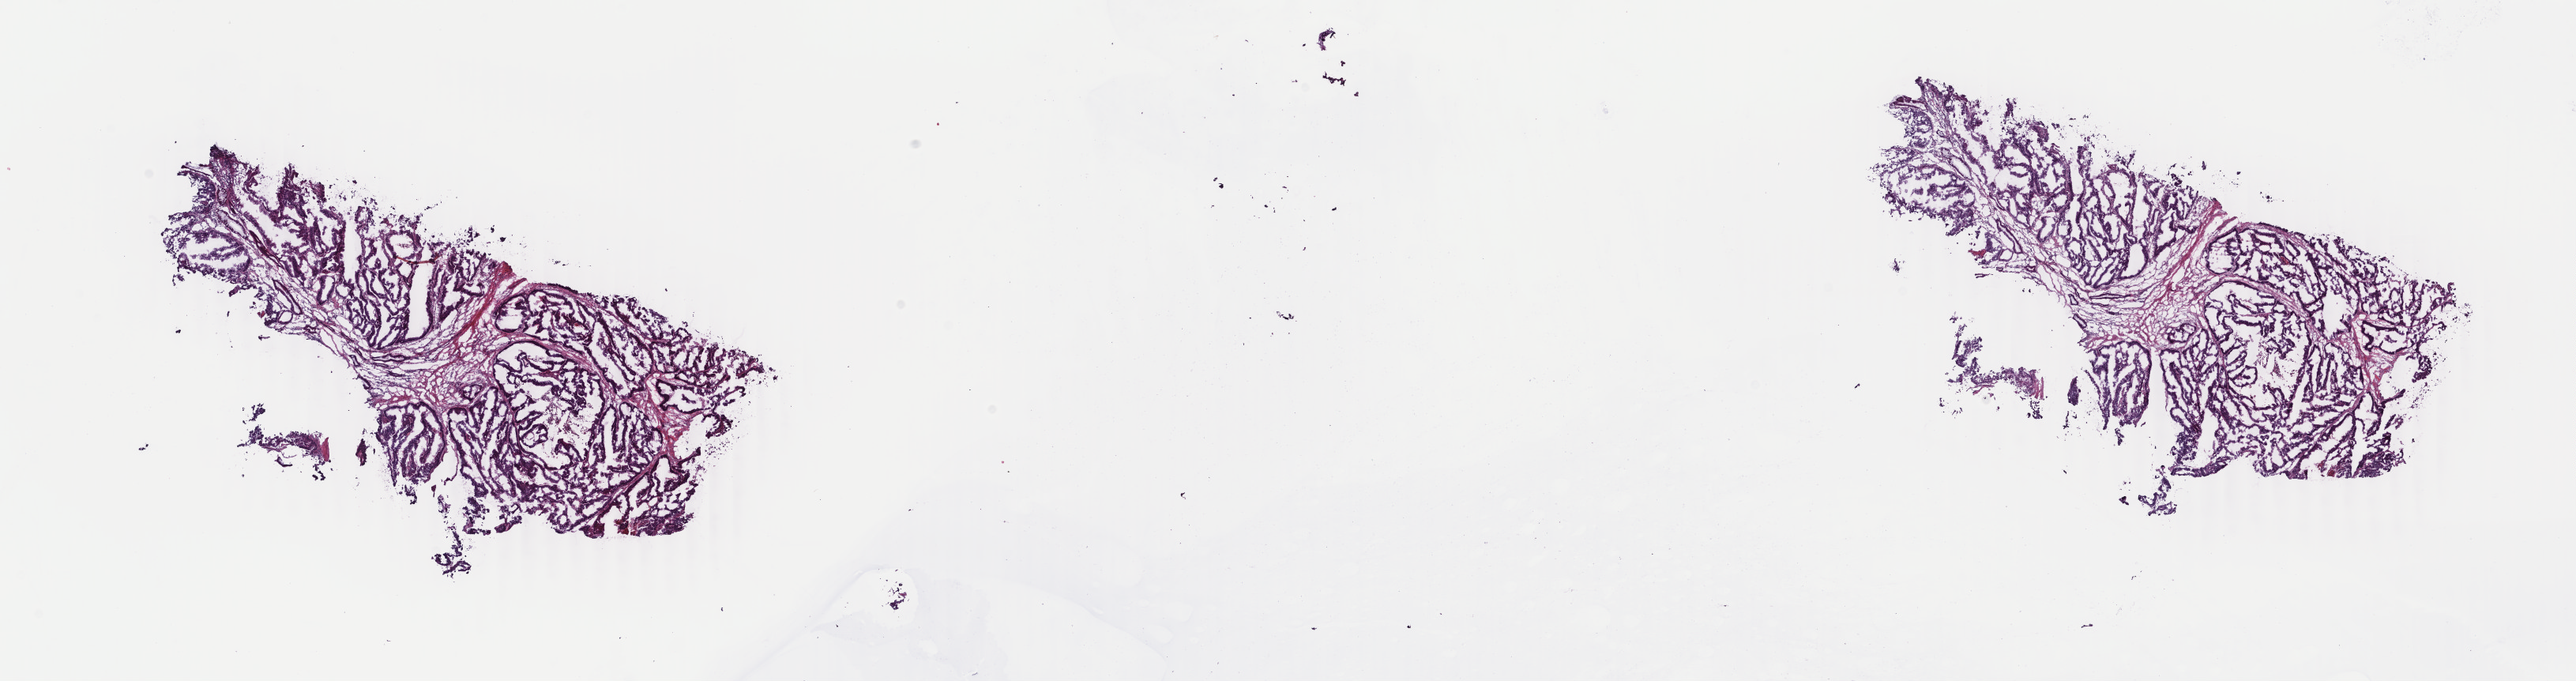
Digitized H&E-stained tissue section (whole slide) — low-resolution overview of the scanned area, about 25.9 x 6.9 mm (from a 40x scan). Frozen section. Colon, primary tumour sample. Male, age 51 years at initial diagnosis. Composition of this section per pathologist review: tumour cells 80%, tumour nuclei 80%, normal cells 7%, stromal cells 10%, necrosis 3%. Infiltration values recorded for this section: lymphocyte infiltration 3%, monocyte infiltration 1%, neutrophil infiltration 0%.
TNM: T3 N2a MX. Diagnosis: Adenocarcinoma, NOS. AJCC pathologic stage: IIIB (7th edition).